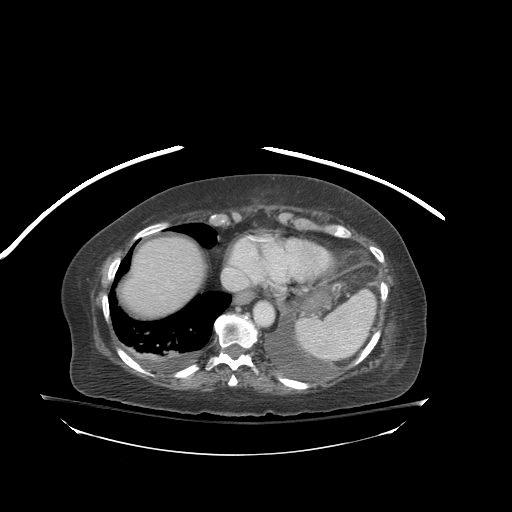
Contrast-enhanced abdominal CT (liver protocol), one axial slice; slice 75 of 81 in the series (ordered by position); 140 kVp; soft-tissue window (W 400 / L 40 HU); 2.5 mm slice thickness; 512 × 512 image matrix, field of view 500 × 500 mm. Case-level facts recorded for this patient, not image findings: diagnosis: hepatocellular carcinoma (patient treated with transarterial chemoembolisation; whether this scan precedes or follows treatment is not stated here); TNM stage (as recorded): Stage-I; Child-Pugh class: B.
Annotated regions visible in this slice (semi-automatic segmentation, software-assisted and operator-edited):
- abdominal aorta: box from (x=255, y=302) to (x=273, y=324) px
- liver parenchyma outside the tumour (the mass and vessels are separate outlines, so this box may not span the whole liver): (x=122, y=236)–(x=204, y=316)